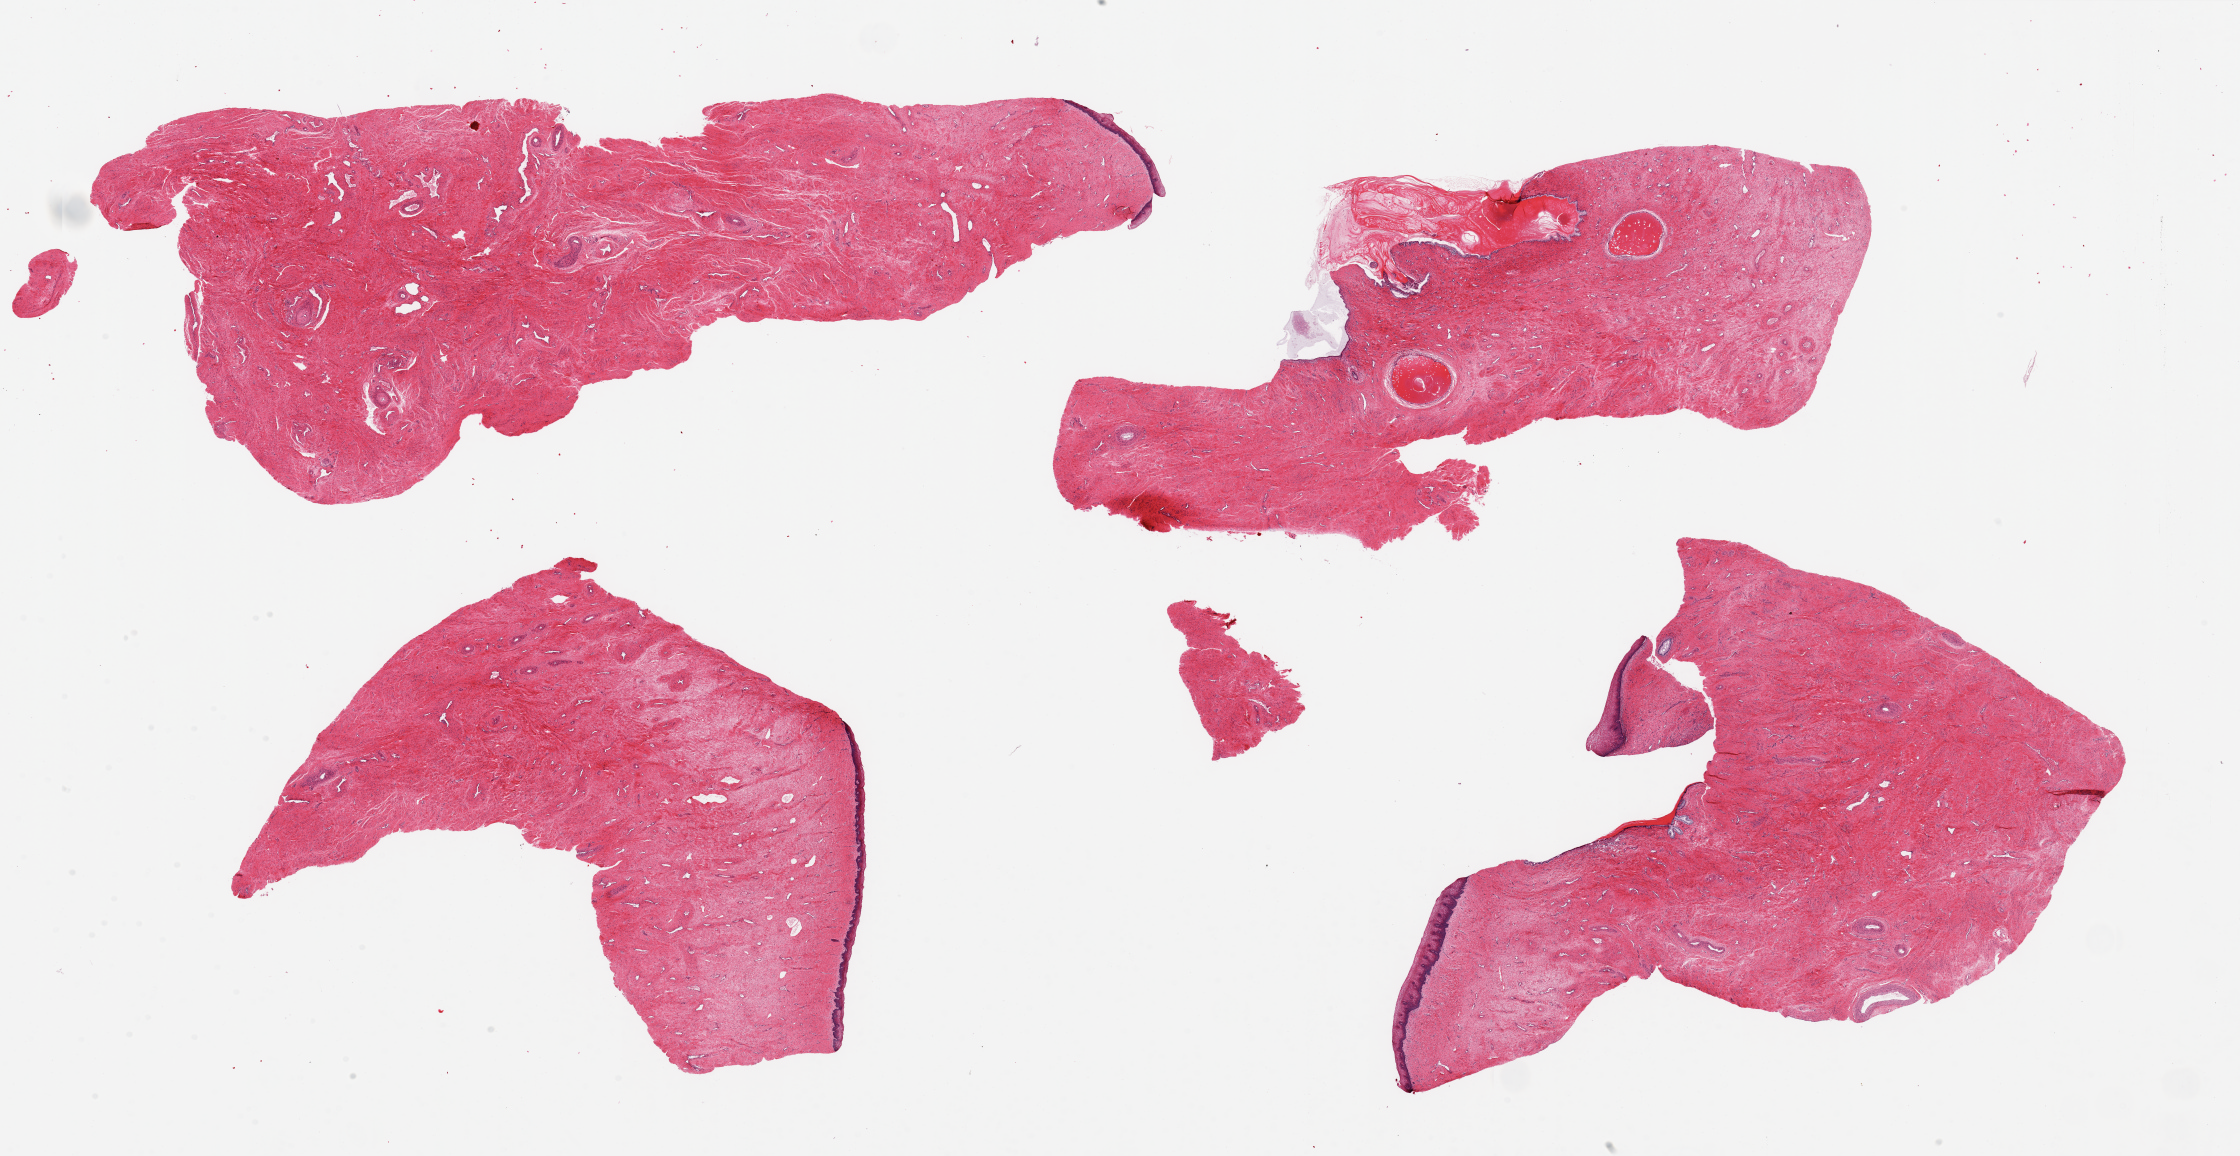
Digitized hematoxylin and eosin (H&E)-stained section, brightfield — low-resolution overview of the scanned area, about 35.4 x 18.3 mm, PAXgene-fixed, paraffin-embedded tissue, target tissue: exocervix, tissue donor sample. Female donor.
• reviewer comment on this tissue sample: 4 aliquots, ~ 12x9mm; 3 show focal squamous mucosa, ~100 microns thick; one with single layer endocervical mucosa, 10 microns thick, en